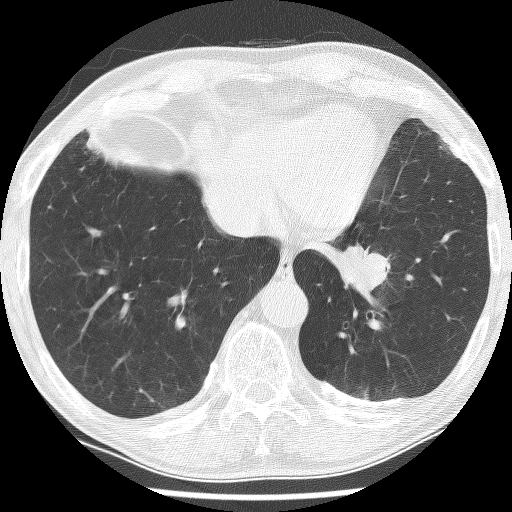
Chest CT (low-dose screening protocol), one axial image, baseline screening round, lung window (W 1500 / L -600 HU), 2.5 mm slice thickness, 120 kVp. Male, age 74 years at enrolment. Current smoker at enrolment.
Lesion marked by an expert reader, bounding box [x1, y1, x2, y2] px = [313, 218, 415, 310]. The exam's reader record, not a measurement of the box and not confirmed to be the same lesion: non-calcified nodule or mass ≥4 mm, left lower lobe, 30 × 27 mm, spiculated (stellate) margins, soft tissue attenuation. Official screen result: positive, change unspecified: nodule(s) >= 4 mm or enlarging nodule(s), mass(es), or other non-specific abnormalities suspicious for lung cancer.